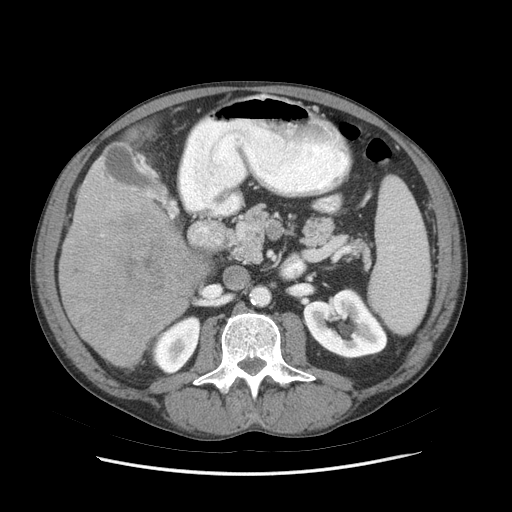
Contrast-enhanced abdominal CT (liver protocol), one axial slice. Slice 29 of 89 in the series (ordered by position). Reconstruction kernel STANDARD. Soft-tissue window (W 400 / L 40 HU). 512 × 512 image matrix, field of view 380 × 380 mm. From the clinical record (not read from this slice): diagnosis: hepatocellular carcinoma (patient treated with transarterial chemoembolisation; whether this scan precedes or follows treatment is not stated here); TNM stage (as recorded): Stage-IIIB; Child-Pugh class: A; tumour differentiation: moderately differentiated; tumour nodularity: multinodular.
Outlined on this slice (semi-automatically segmented with operator editing):
- liver parenchyma outside the tumour (the mass and vessels are separate outlines, so this box may not span the whole liver): box from (x=58, y=156) to (x=169, y=366) px
- mass: (x=61, y=205)–(x=202, y=366)